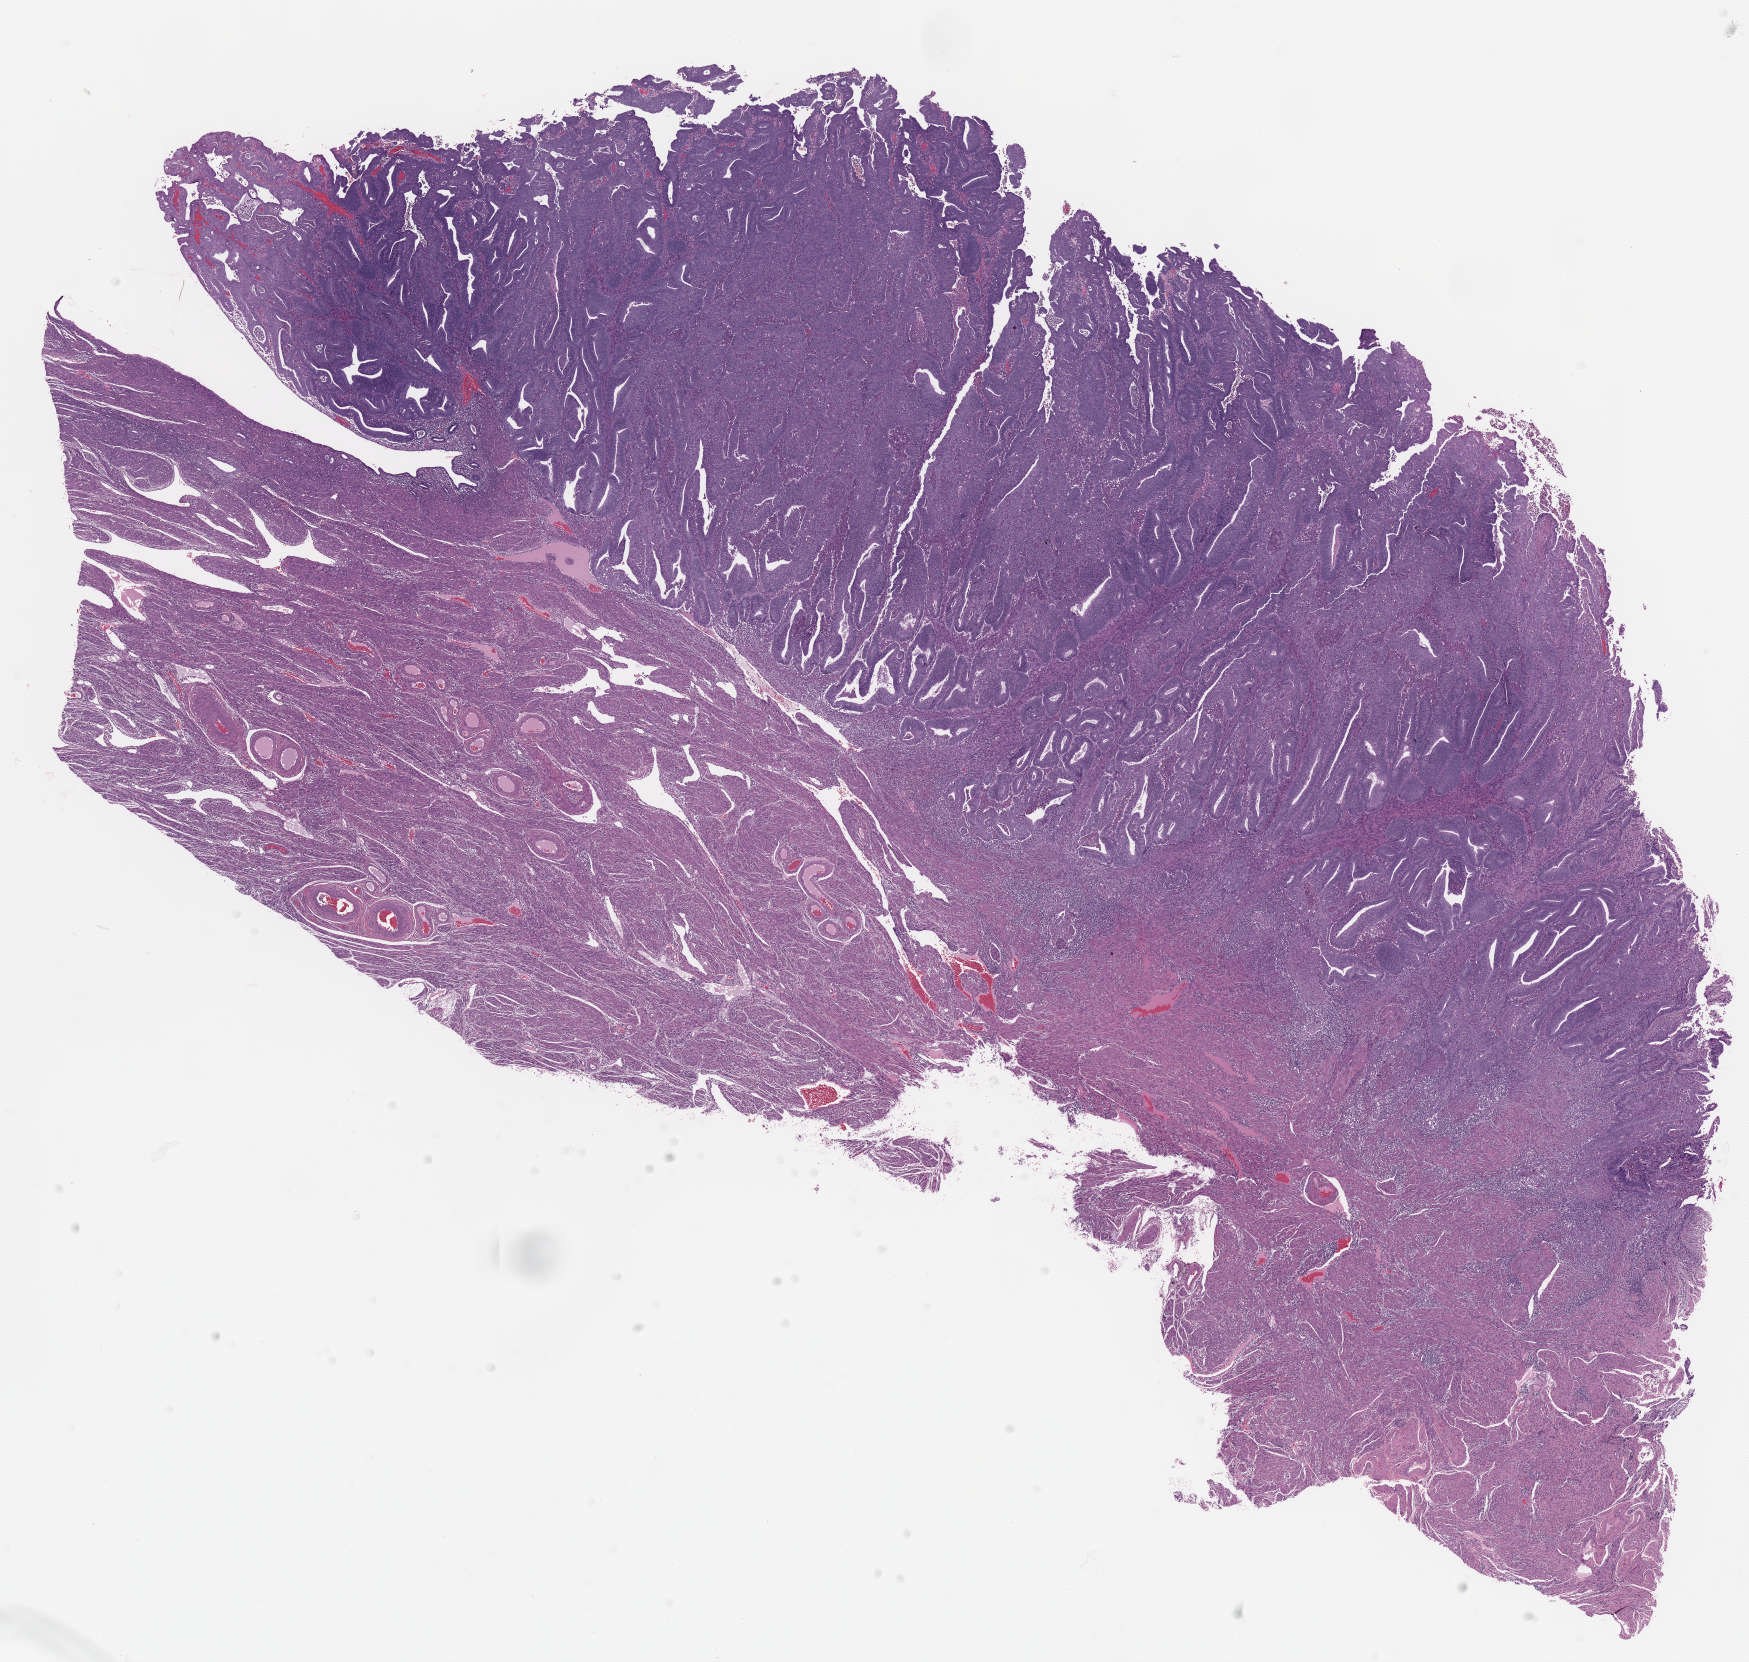
Hematoxylin and eosin (H&E) stained whole-slide image — whole scanned area (about 14.0 x 13.3 mm, slide scanned at 20x) shown as a low-resolution overview; FFPE section; uterus, primary tumour sample. Female patient; age at initial diagnosis 55 years. Histologic grade: G3 (poorly differentiated).
FIGO stage: IB. Lymph nodes positive (case pathology): 0 of 21 examined. Diagnosis: Endometrioid adenocarcinoma, NOS (endometrium).